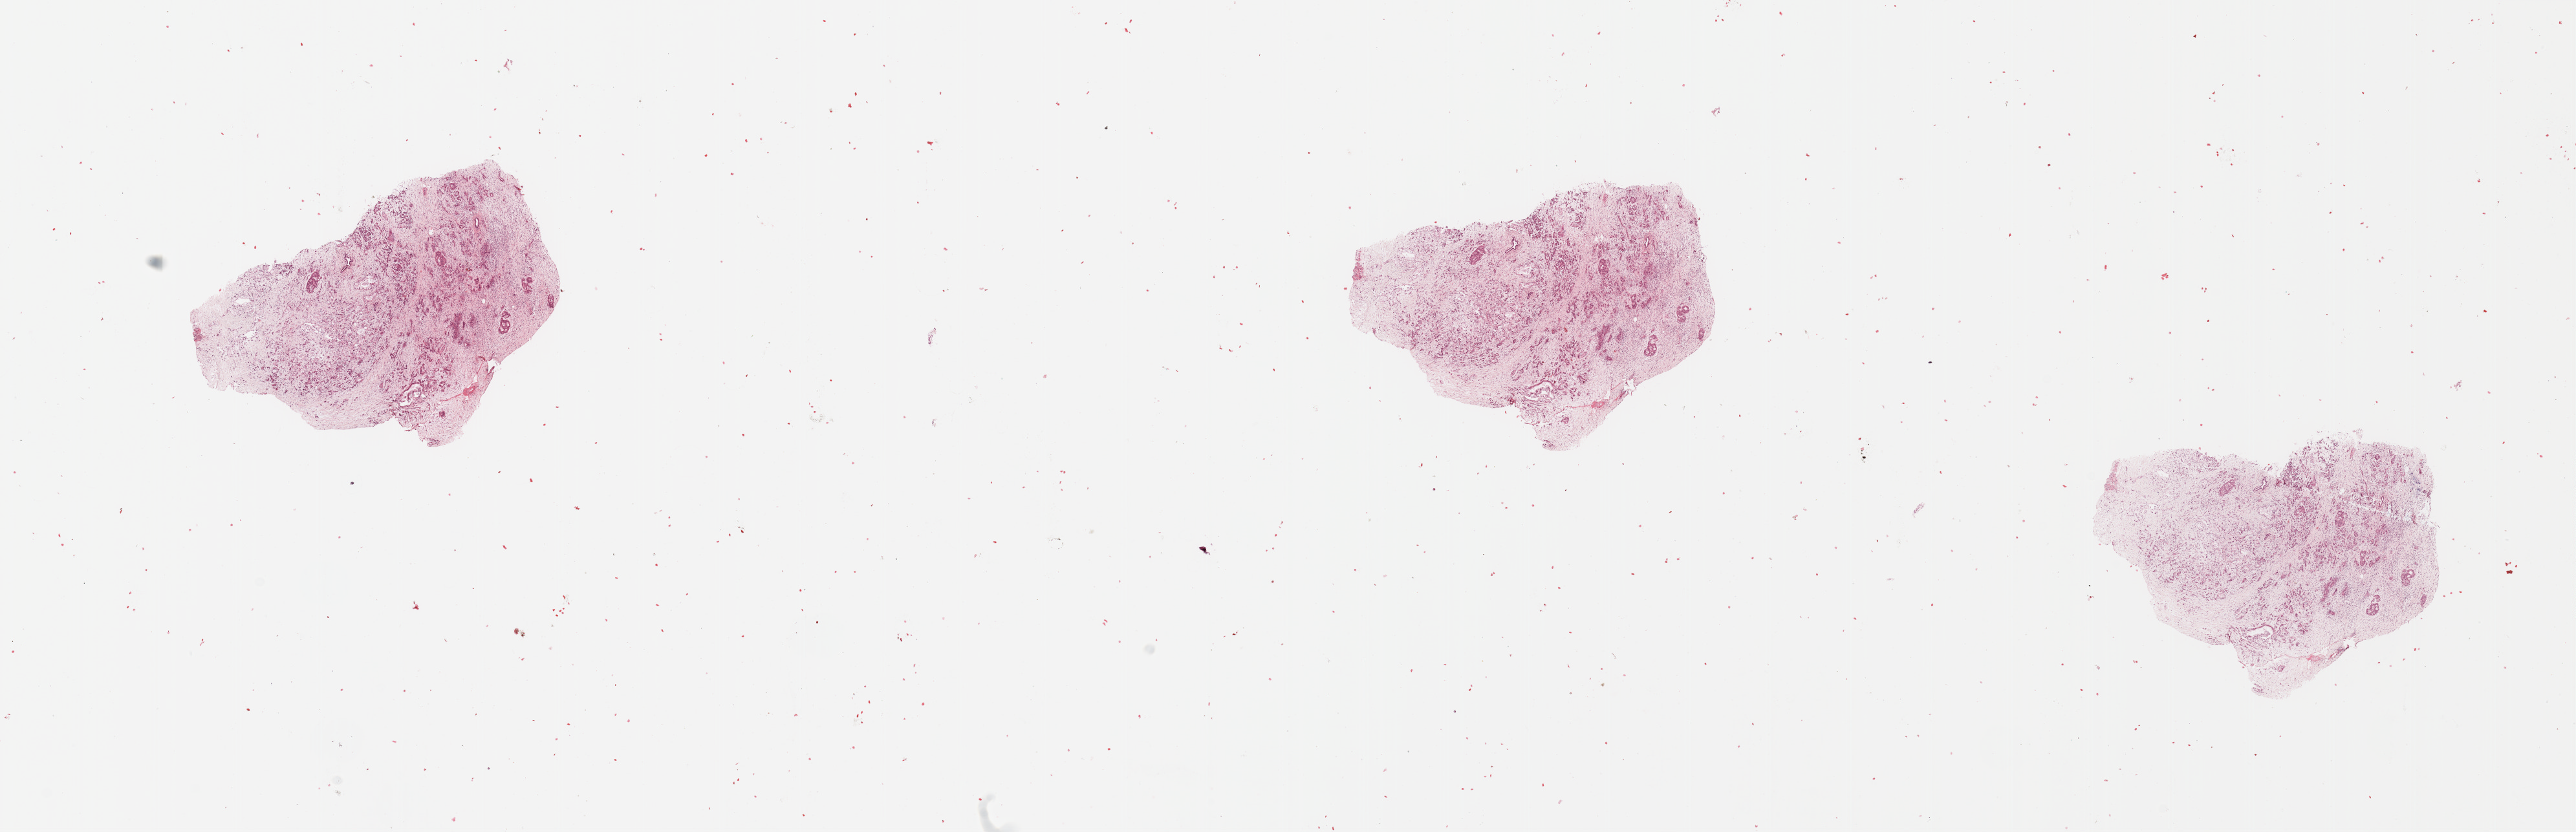
Whole-slide histology image, H&E, shown as a low-resolution overview of the whole scanned area (about 31.5 x 10.2 mm, from a 20x scan); pancreas, tumour tissue. Patient: male, age 62 years.
Patient diagnosis (cohort enrolment): ductal adenocarcinoma (pancreas). Primary tumour site (as recorded): head.